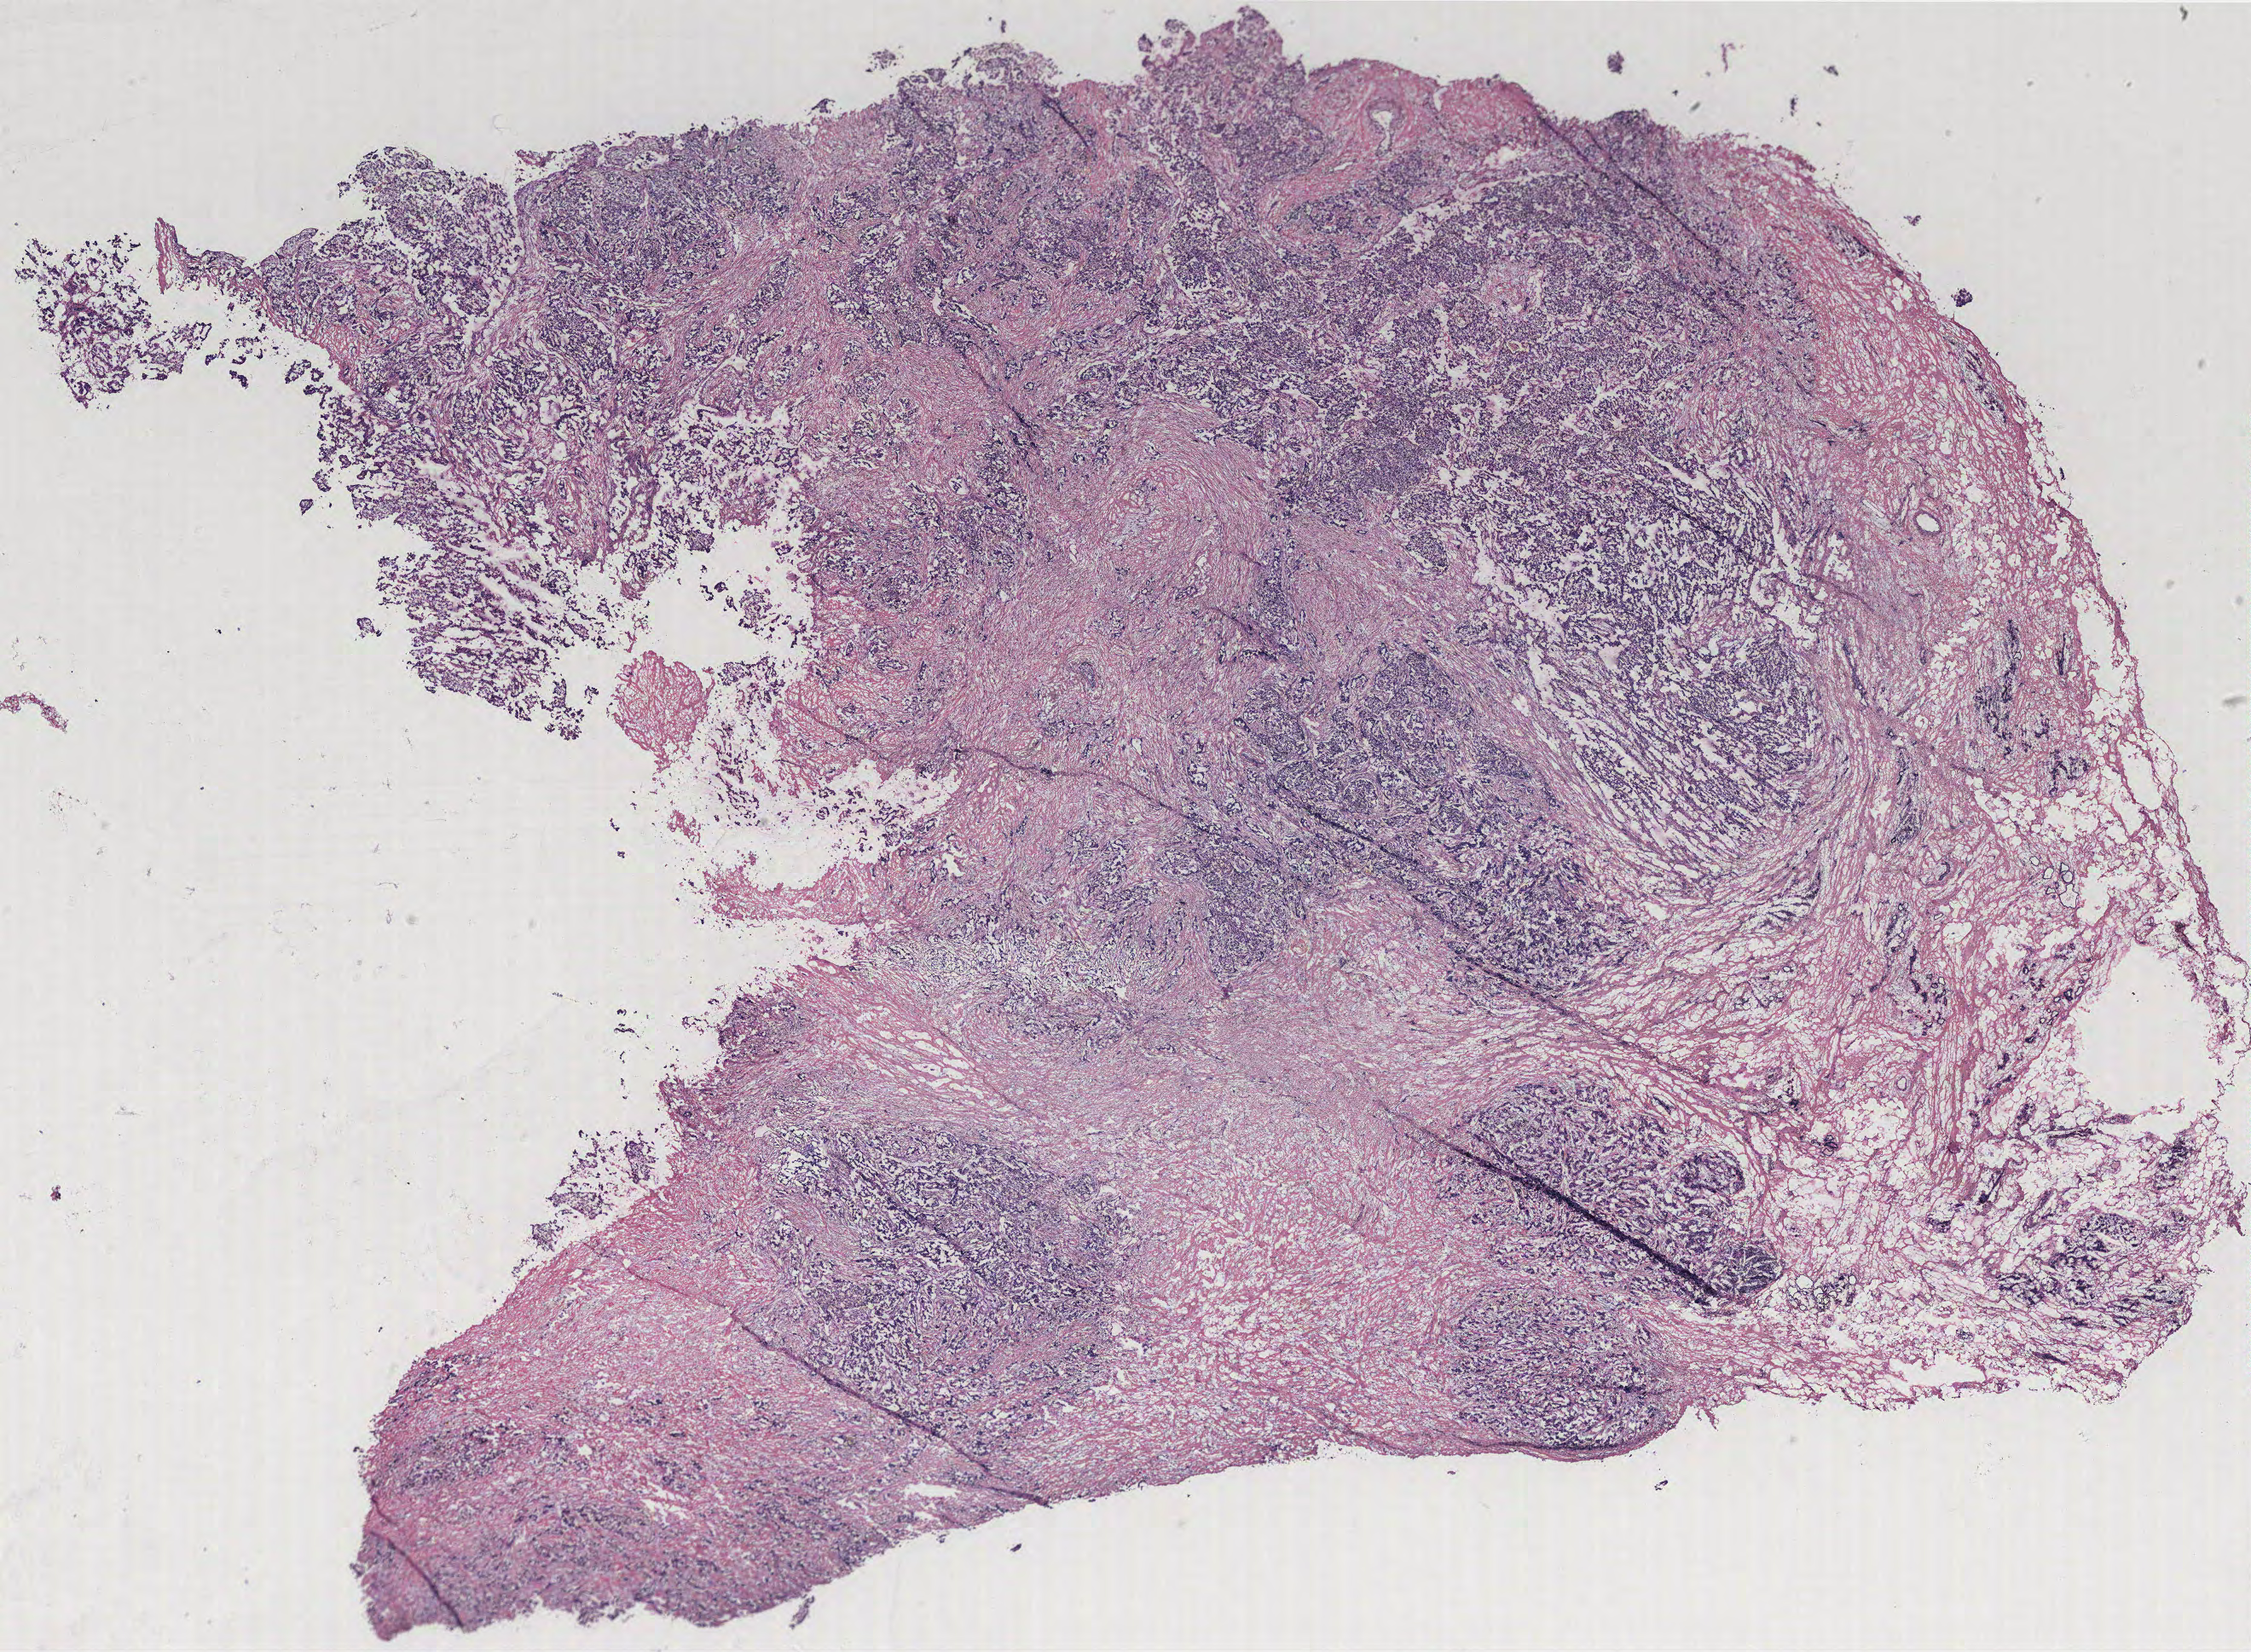
Whole-slide histology image, Hematoxylin and eosin (H&E) stained — whole scanned area (about 21.1 x 15.5 mm) shown as a low-resolution overview; tumour tissue sample, breast. Female, 52 y/o.
- diagnosis: Infiltrating duct carcinoma, NOS
- AJCC pathologic stage: IIB